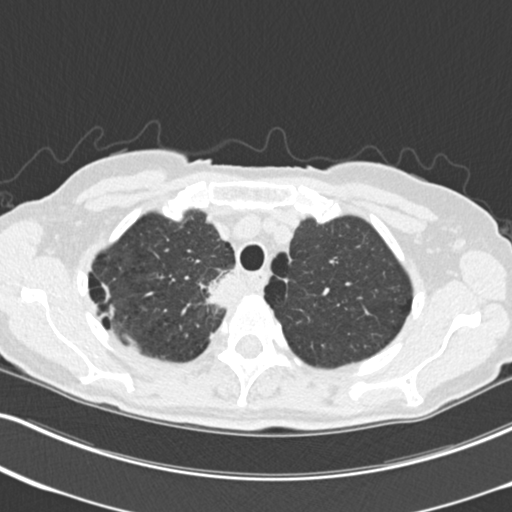
Low-dose screening chest CT, one axial slice. Position 182 of 226 along the scan axis. 120 kVp. Lung window (W 1500 / L -600 HU). 2 mm slice thickness. 512 × 512 image matrix.
Annotated regions visible in this slice (manually delineated by an expert):
- lesion 1 (tumor, mediastinum): bounding box <206,272,236,308> (left, top, right, bottom; pixels)